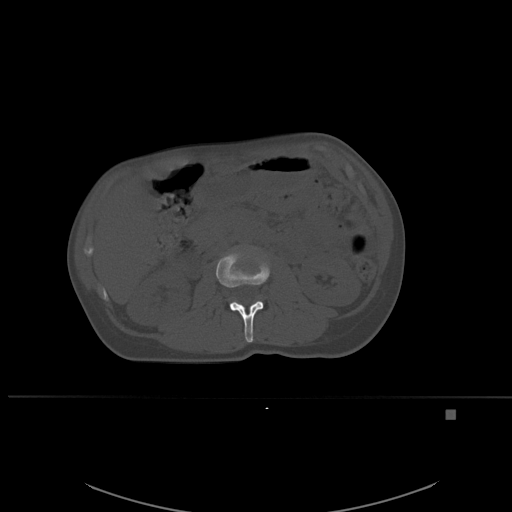
CT including the spine, one axial slice; position 230 of 537 along the scan axis; bone window (W 1800 / L 400 HU); 1.5 mm slice thickness; 512 × 512 image matrix. Female patient, age 45 years. Case-level facts recorded for this patient, not image findings: primary cancer: lung.
Outlined on this slice (semi-automatic segmentation, software-assisted and operator-edited):
- L2 vertebra: bounding box <216,249,270,342> (left, top, right, bottom; pixels)